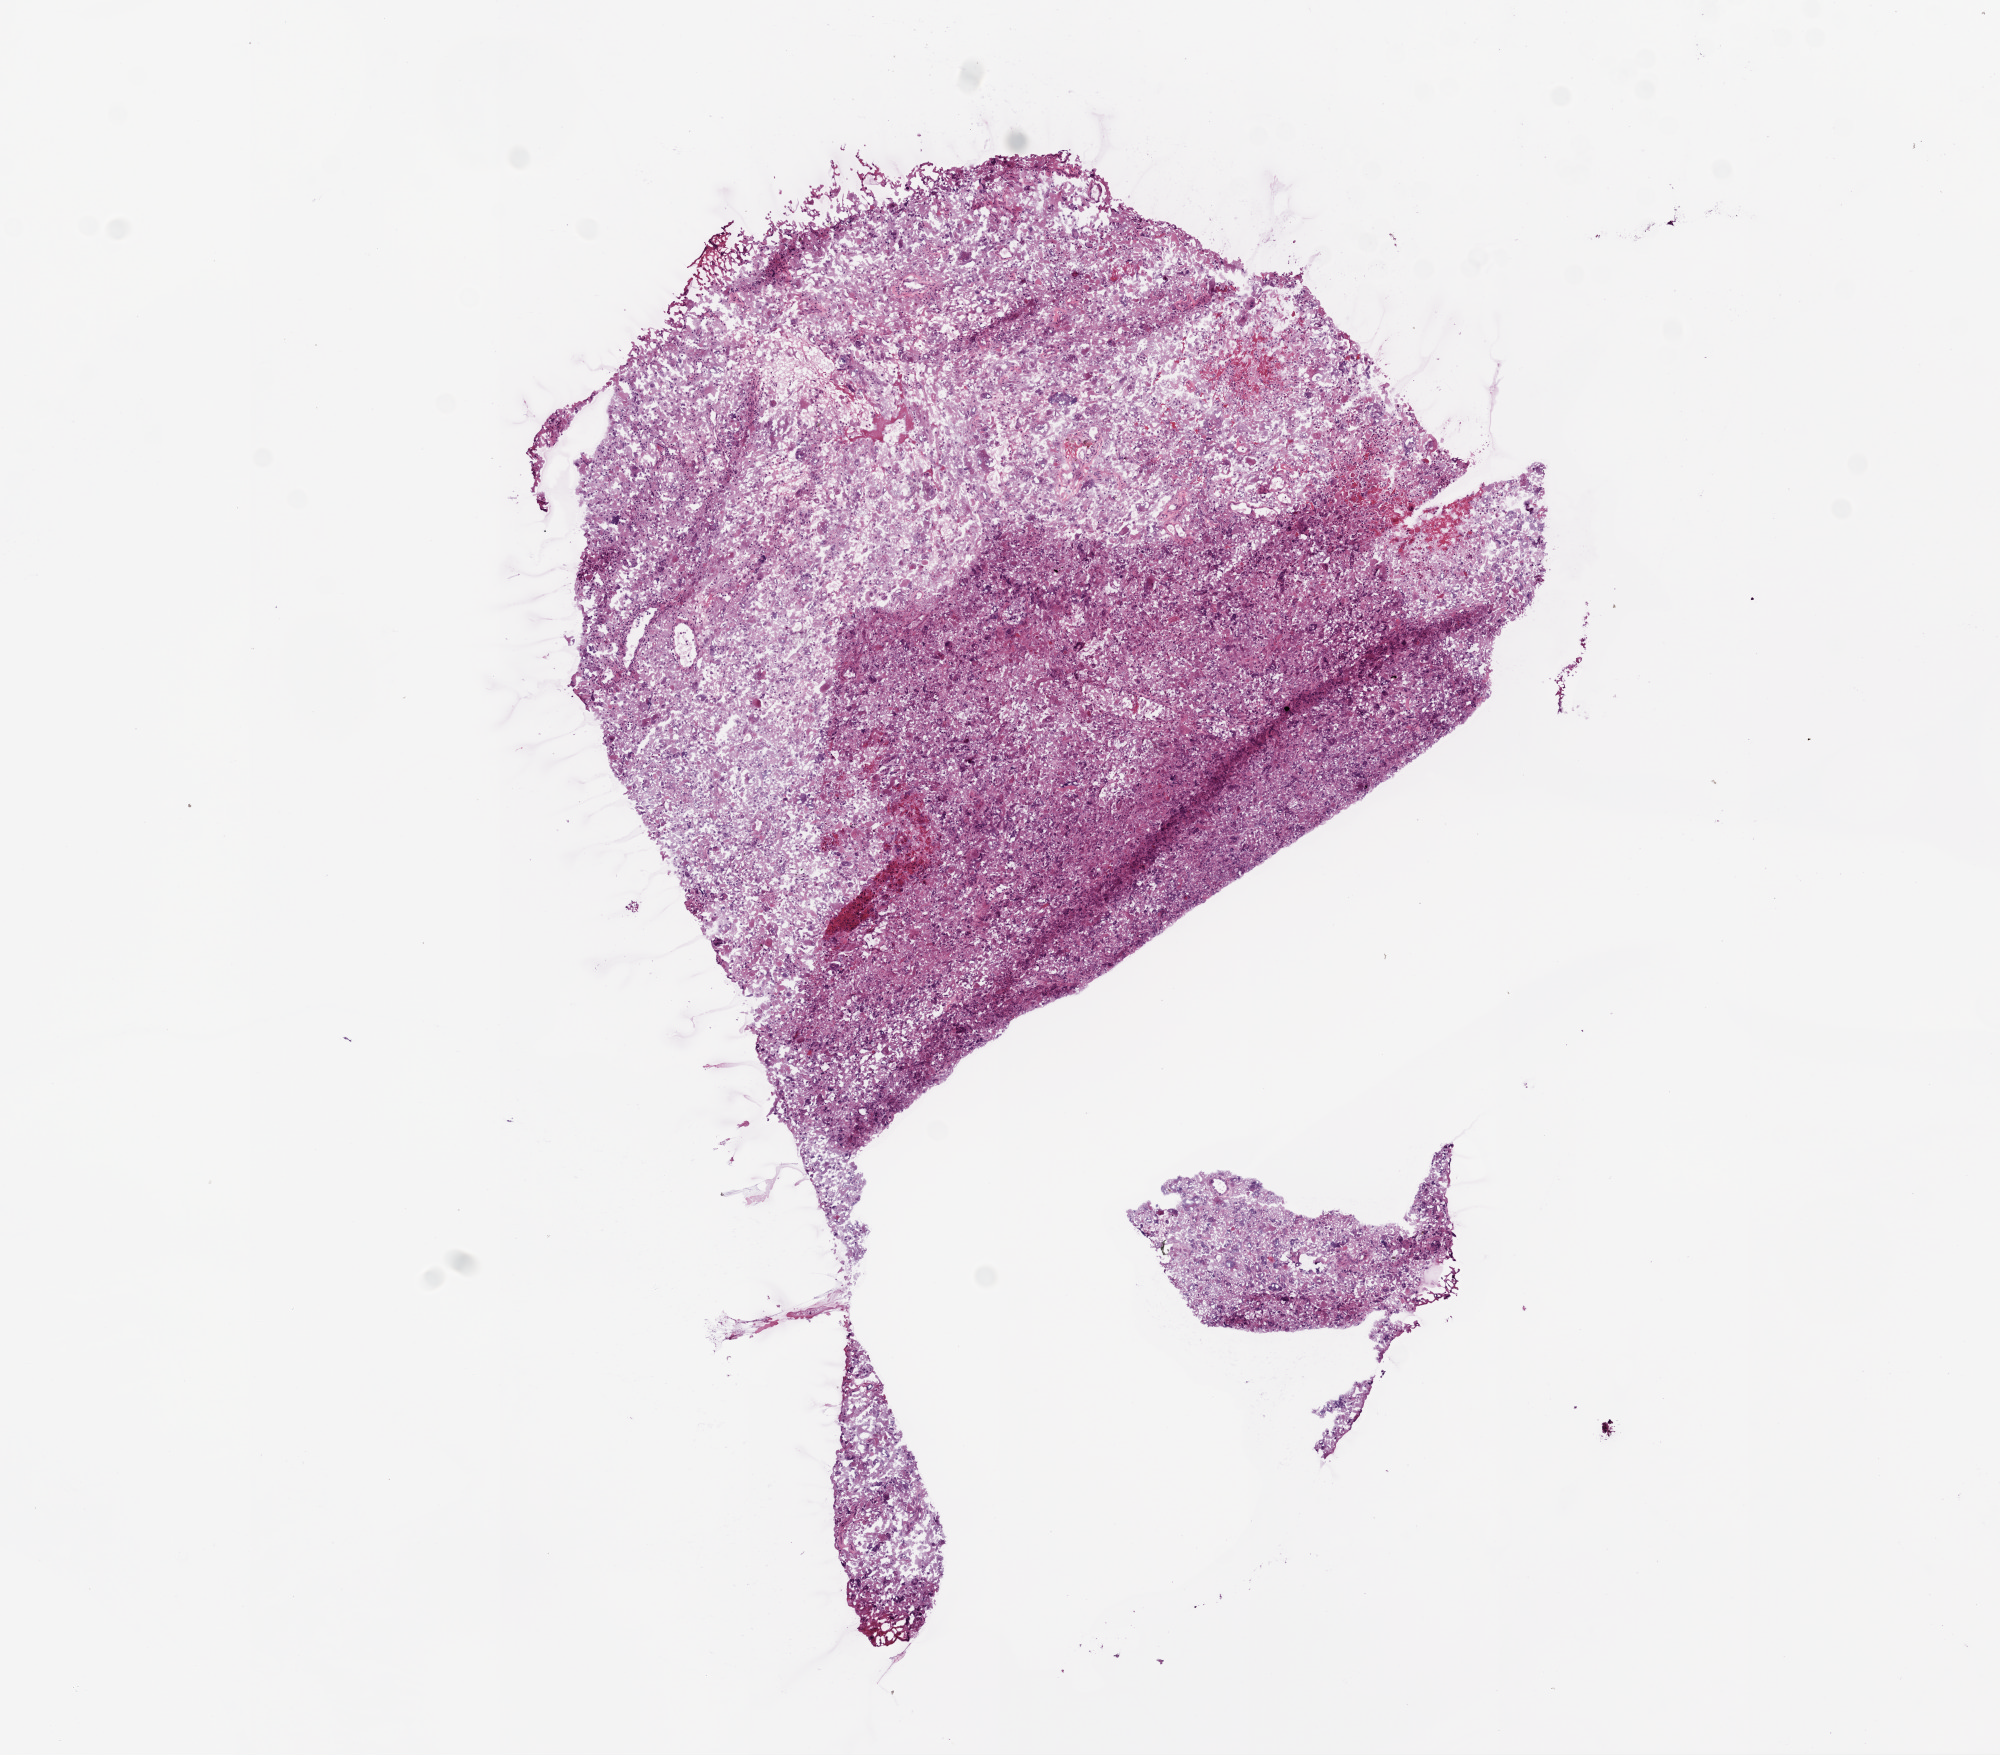
Hematoxylin and eosin (H&E) stained whole-slide image — whole scanned area (about 8.0 x 7.0 mm, acquisition: 20x scan) shown as a low-resolution overview, frozen section from the bottom of the tissue portion, primary tumour sample from the brain. Male, age 37 years at initial diagnosis. Pathologist review of this section (percent, as recorded): tumour cells 95%, tumour nuclei 80%.
Histologic diagnosis: Glioblastoma.